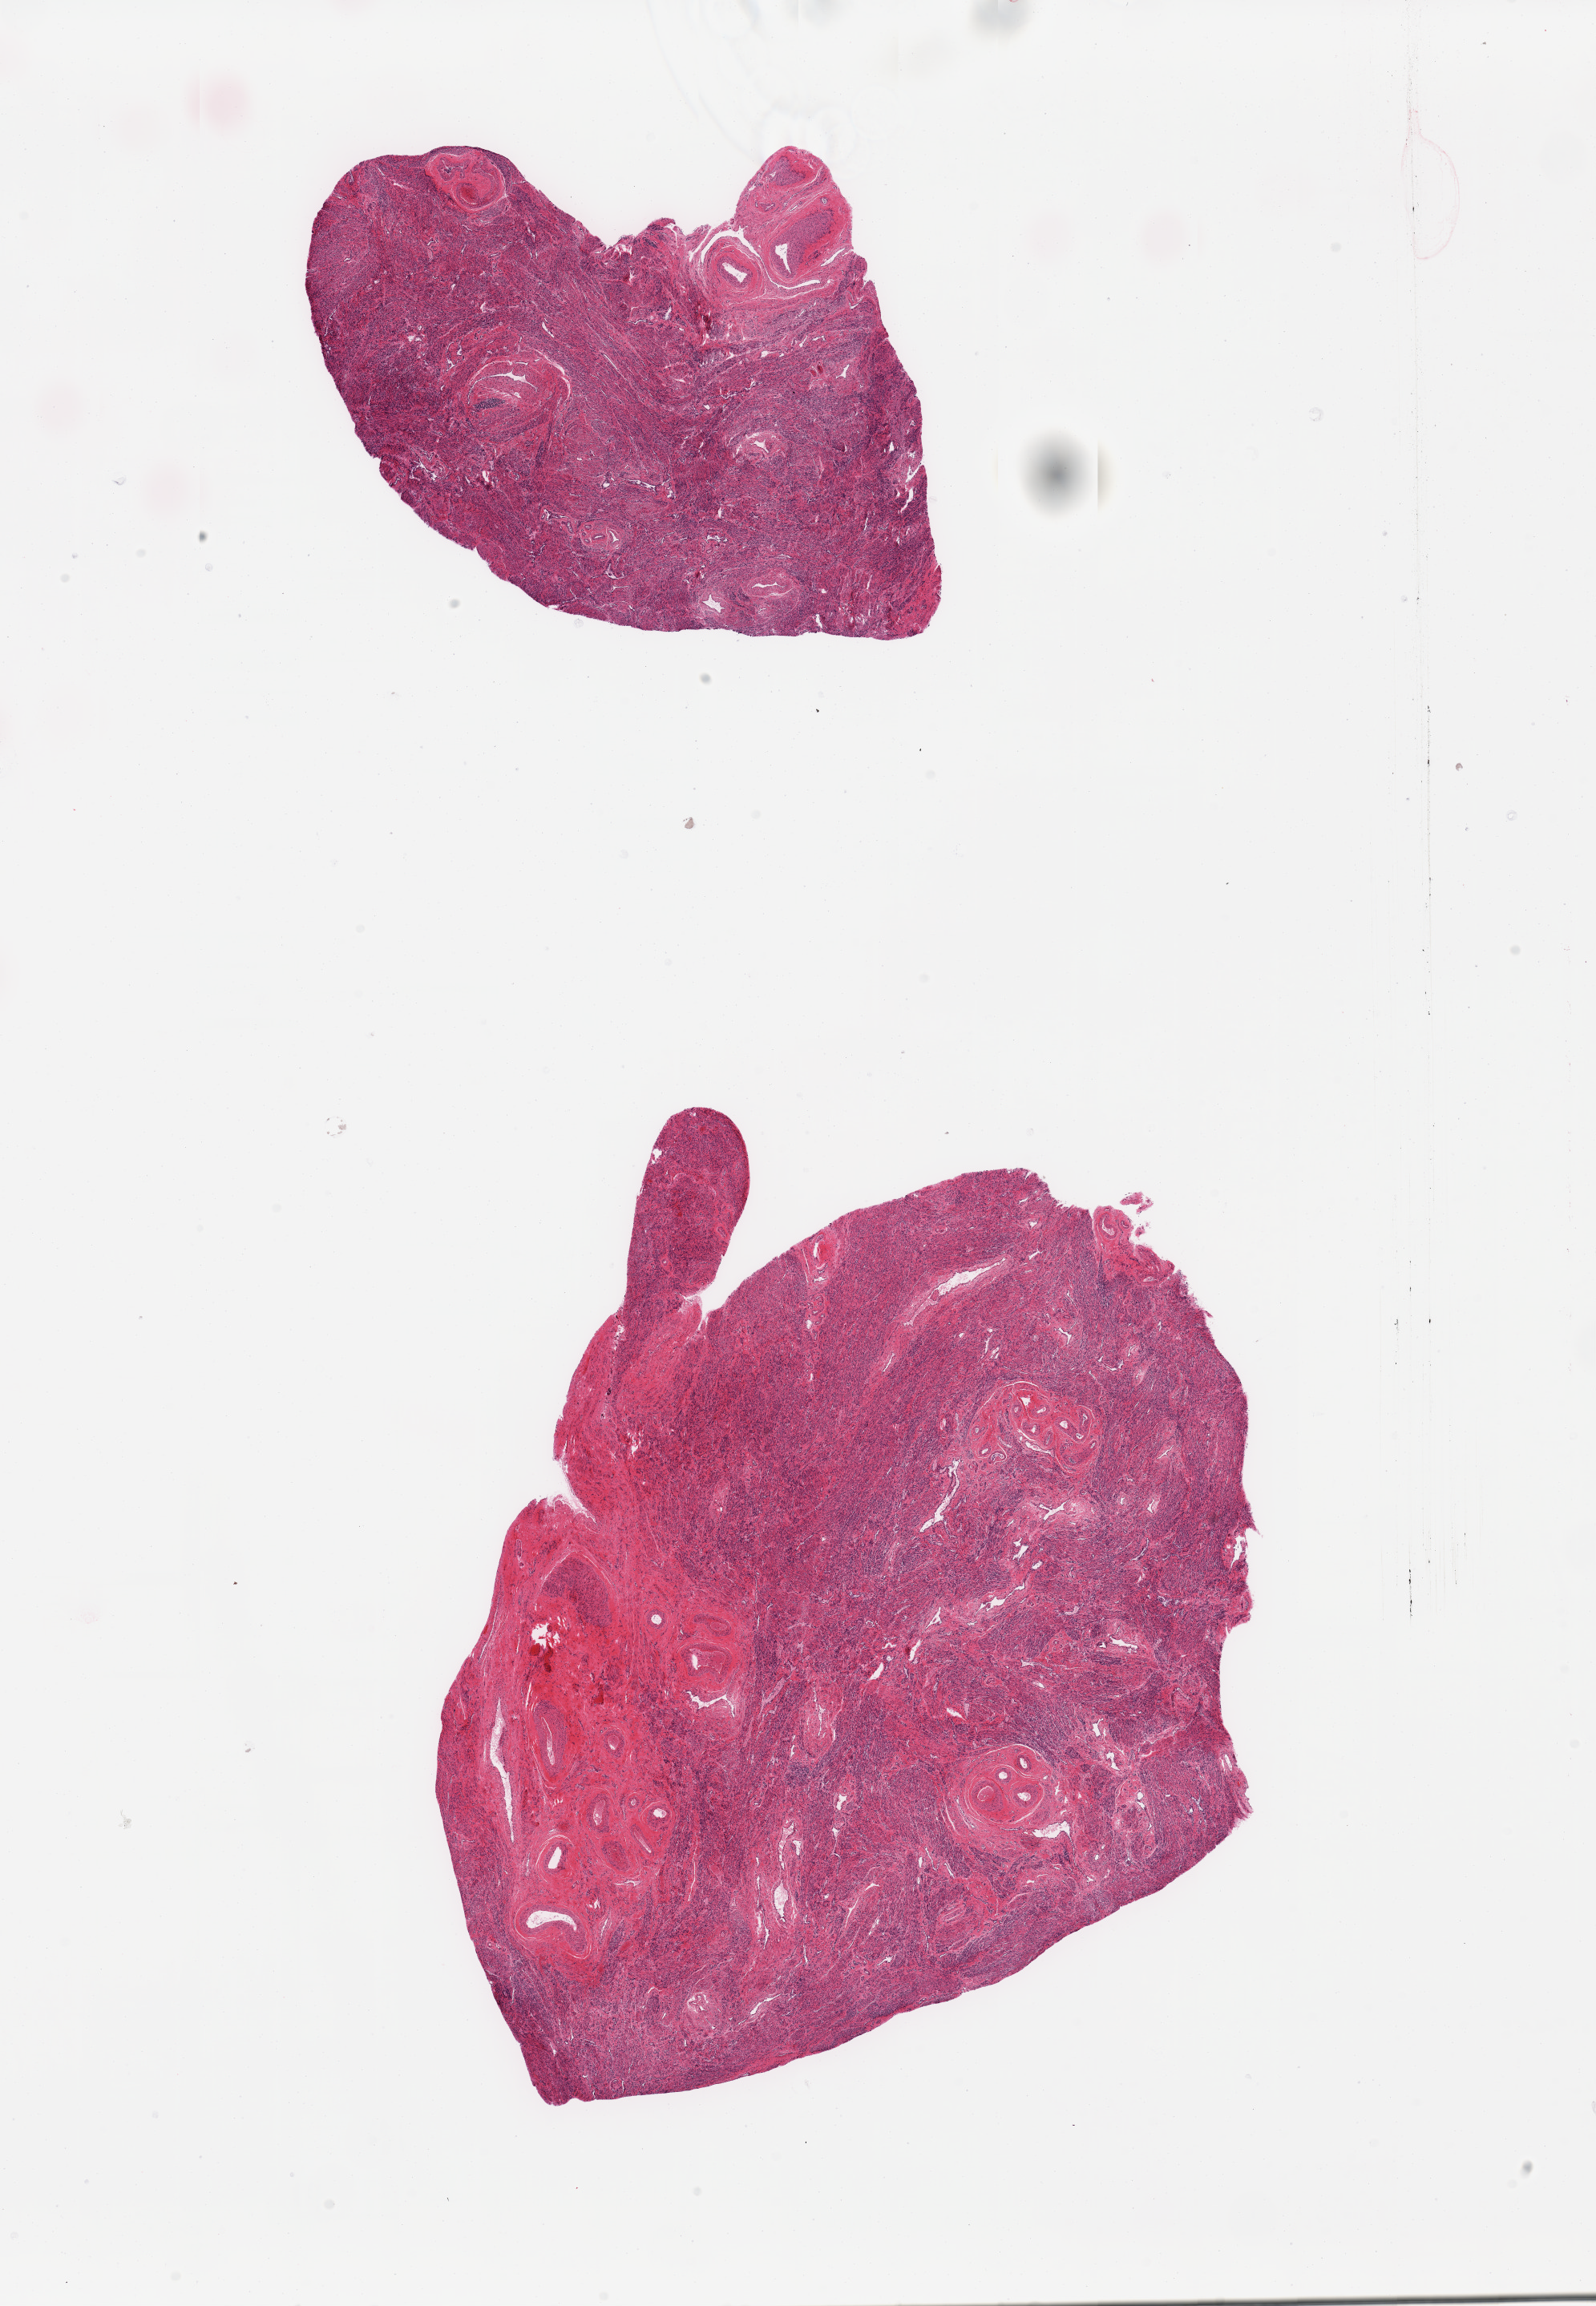
Whole-slide image, haematoxylin and eosin stain, whole scanned area (about 15.8 x 22.8 mm) shown as a low-resolution overview, PAXgene-fixed, paraffin-embedded tissue, sampled site (target tissue): uterus, tissue donor sample. Donor: female.
- review note (as recorded): 2 pieces; myometrium only, no endometrium [in these cuts]